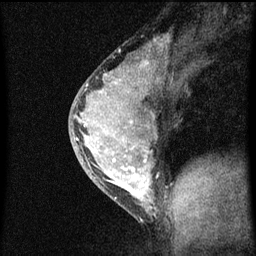
Breast MRI (dynamic contrast-enhanced), one sagittal slice. Position 37 of 60 along the scan axis. Dynamic contrast-enhanced series, image 2 of 3 at this slice position (ordered by acquisition). 1.5 T. TE 4.2 ms, TR 8 ms. 2 mm slice thickness. 256 × 256 image matrix, field of view 180 × 180 mm. Patient: female, 33 years.
Structures marked on this image (semi-automatic segmentation, software-assisted and operator-edited):
- analysis volume of interest (the breast-tissue region the enhancement analysis was run in; not a lesion): bounding box (x1, y1, x2, y2) in pixels: (69, 56, 167, 213)
- tumour enhancement mask (voxels above the 70 % enhancement threshold inside the analysis volume of interest): (78, 62, 153, 207)